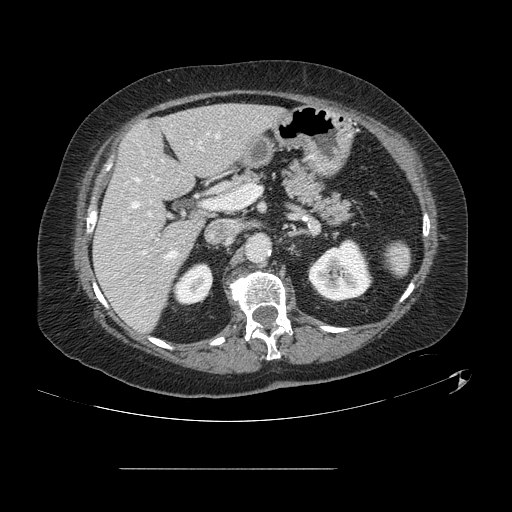
Contrast-enhanced abdominal CT, one axial slice. Position 66 of 148 along the scan axis. Intravenous contrast given. Soft-tissue window (W 400 / L 40 HU). 2.5 mm slice thickness. 512 × 512 image matrix, field of view 439 × 439 mm. Female patient, age 75 years. From the clinical record (not read from this slice): diagnosis: colorectal cancer liver metastases, imaged before liver resection; multiple liver metastases: no; largest metastasis: 2.4 cm; chemotherapy before resection: no.
Outlined on this slice (manually delineated by an expert):
- hepatic veins: bounding box [x1, y1, x2, y2] px = [131, 135, 219, 259]
- liver: [94, 105, 283, 332]
- planned liver remnant (the part of the liver to remain after resection): [94, 105, 283, 332]
- portal vein (with intrahepatic branches): [132, 202, 209, 254]